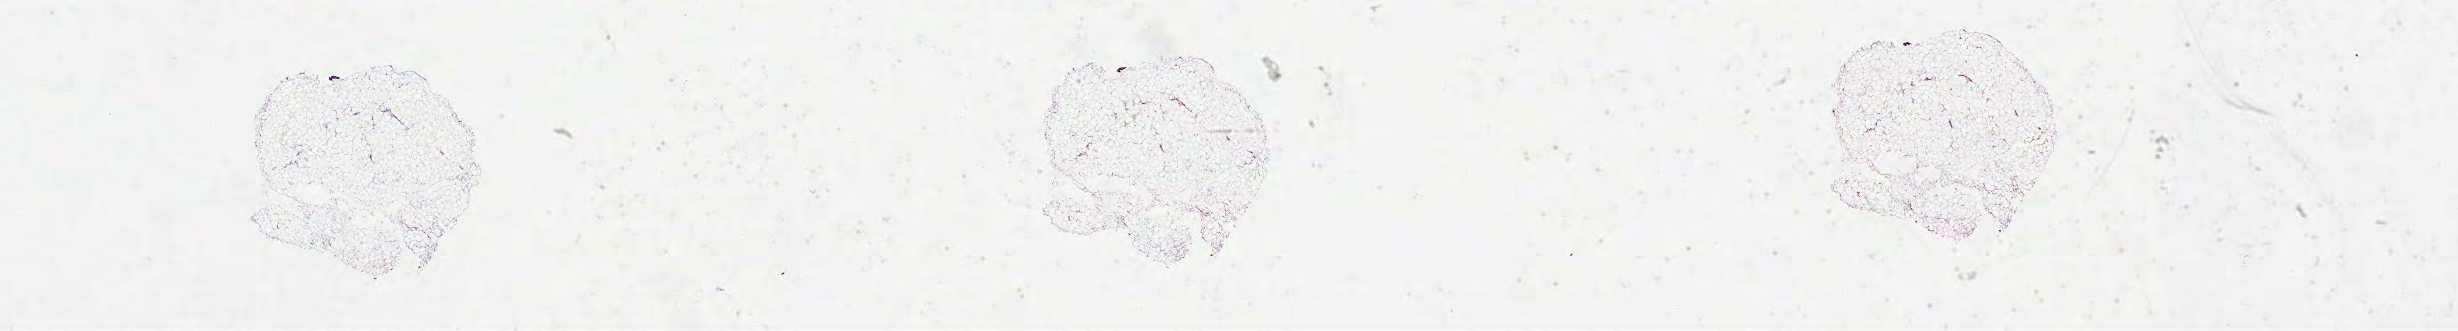
Whole-slide histology image, Hematoxylin and eosin (H&E) stained — low-resolution overview of the scanned area, about 39.6 x 5.3 mm (acquisition: 40x scan); formalin-fixed paraffin-embedded (FFPE) diagnostic section; sample: primary tumour, colon. Male patient; age at initial diagnosis 78 years.
Pathologic diagnosis: Adenocarcinoma, NOS. AJCC pathologic stage: IIA (6th edition). TNM: T3 N0 MX. Lymph nodes positive (case pathology): 0 of 11 examined.